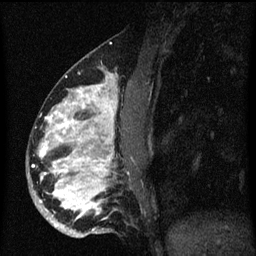
Breast MRI (dynamic contrast-enhanced), one sagittal slice. Slice 25 of 60 in the series (ordered by position). Dynamic contrast-enhanced series, image 2 of 3 at this slice position (ordered by acquisition). 1.5 T. TE 4.2 ms, TR 8.4 ms. 256 × 256 image matrix, field of view 180 × 180 mm. Patient: female, 34 years. Case-level facts recorded for this patient, not image findings: setting: breast cancer imaged before/during neoadjuvant chemotherapy; receptor status: HR-positive, HER2-negative.
Outlined on this slice (semi-automatic segmentation, software-assisted and operator-edited):
- analysis volume of interest (the breast-tissue region the enhancement analysis was run in; not a lesion): box from (x=28, y=58) to (x=135, y=239) px
- tumour enhancement mask (voxels above the 70 % enhancement threshold inside the analysis volume of interest): (x=38, y=78)–(x=117, y=231)